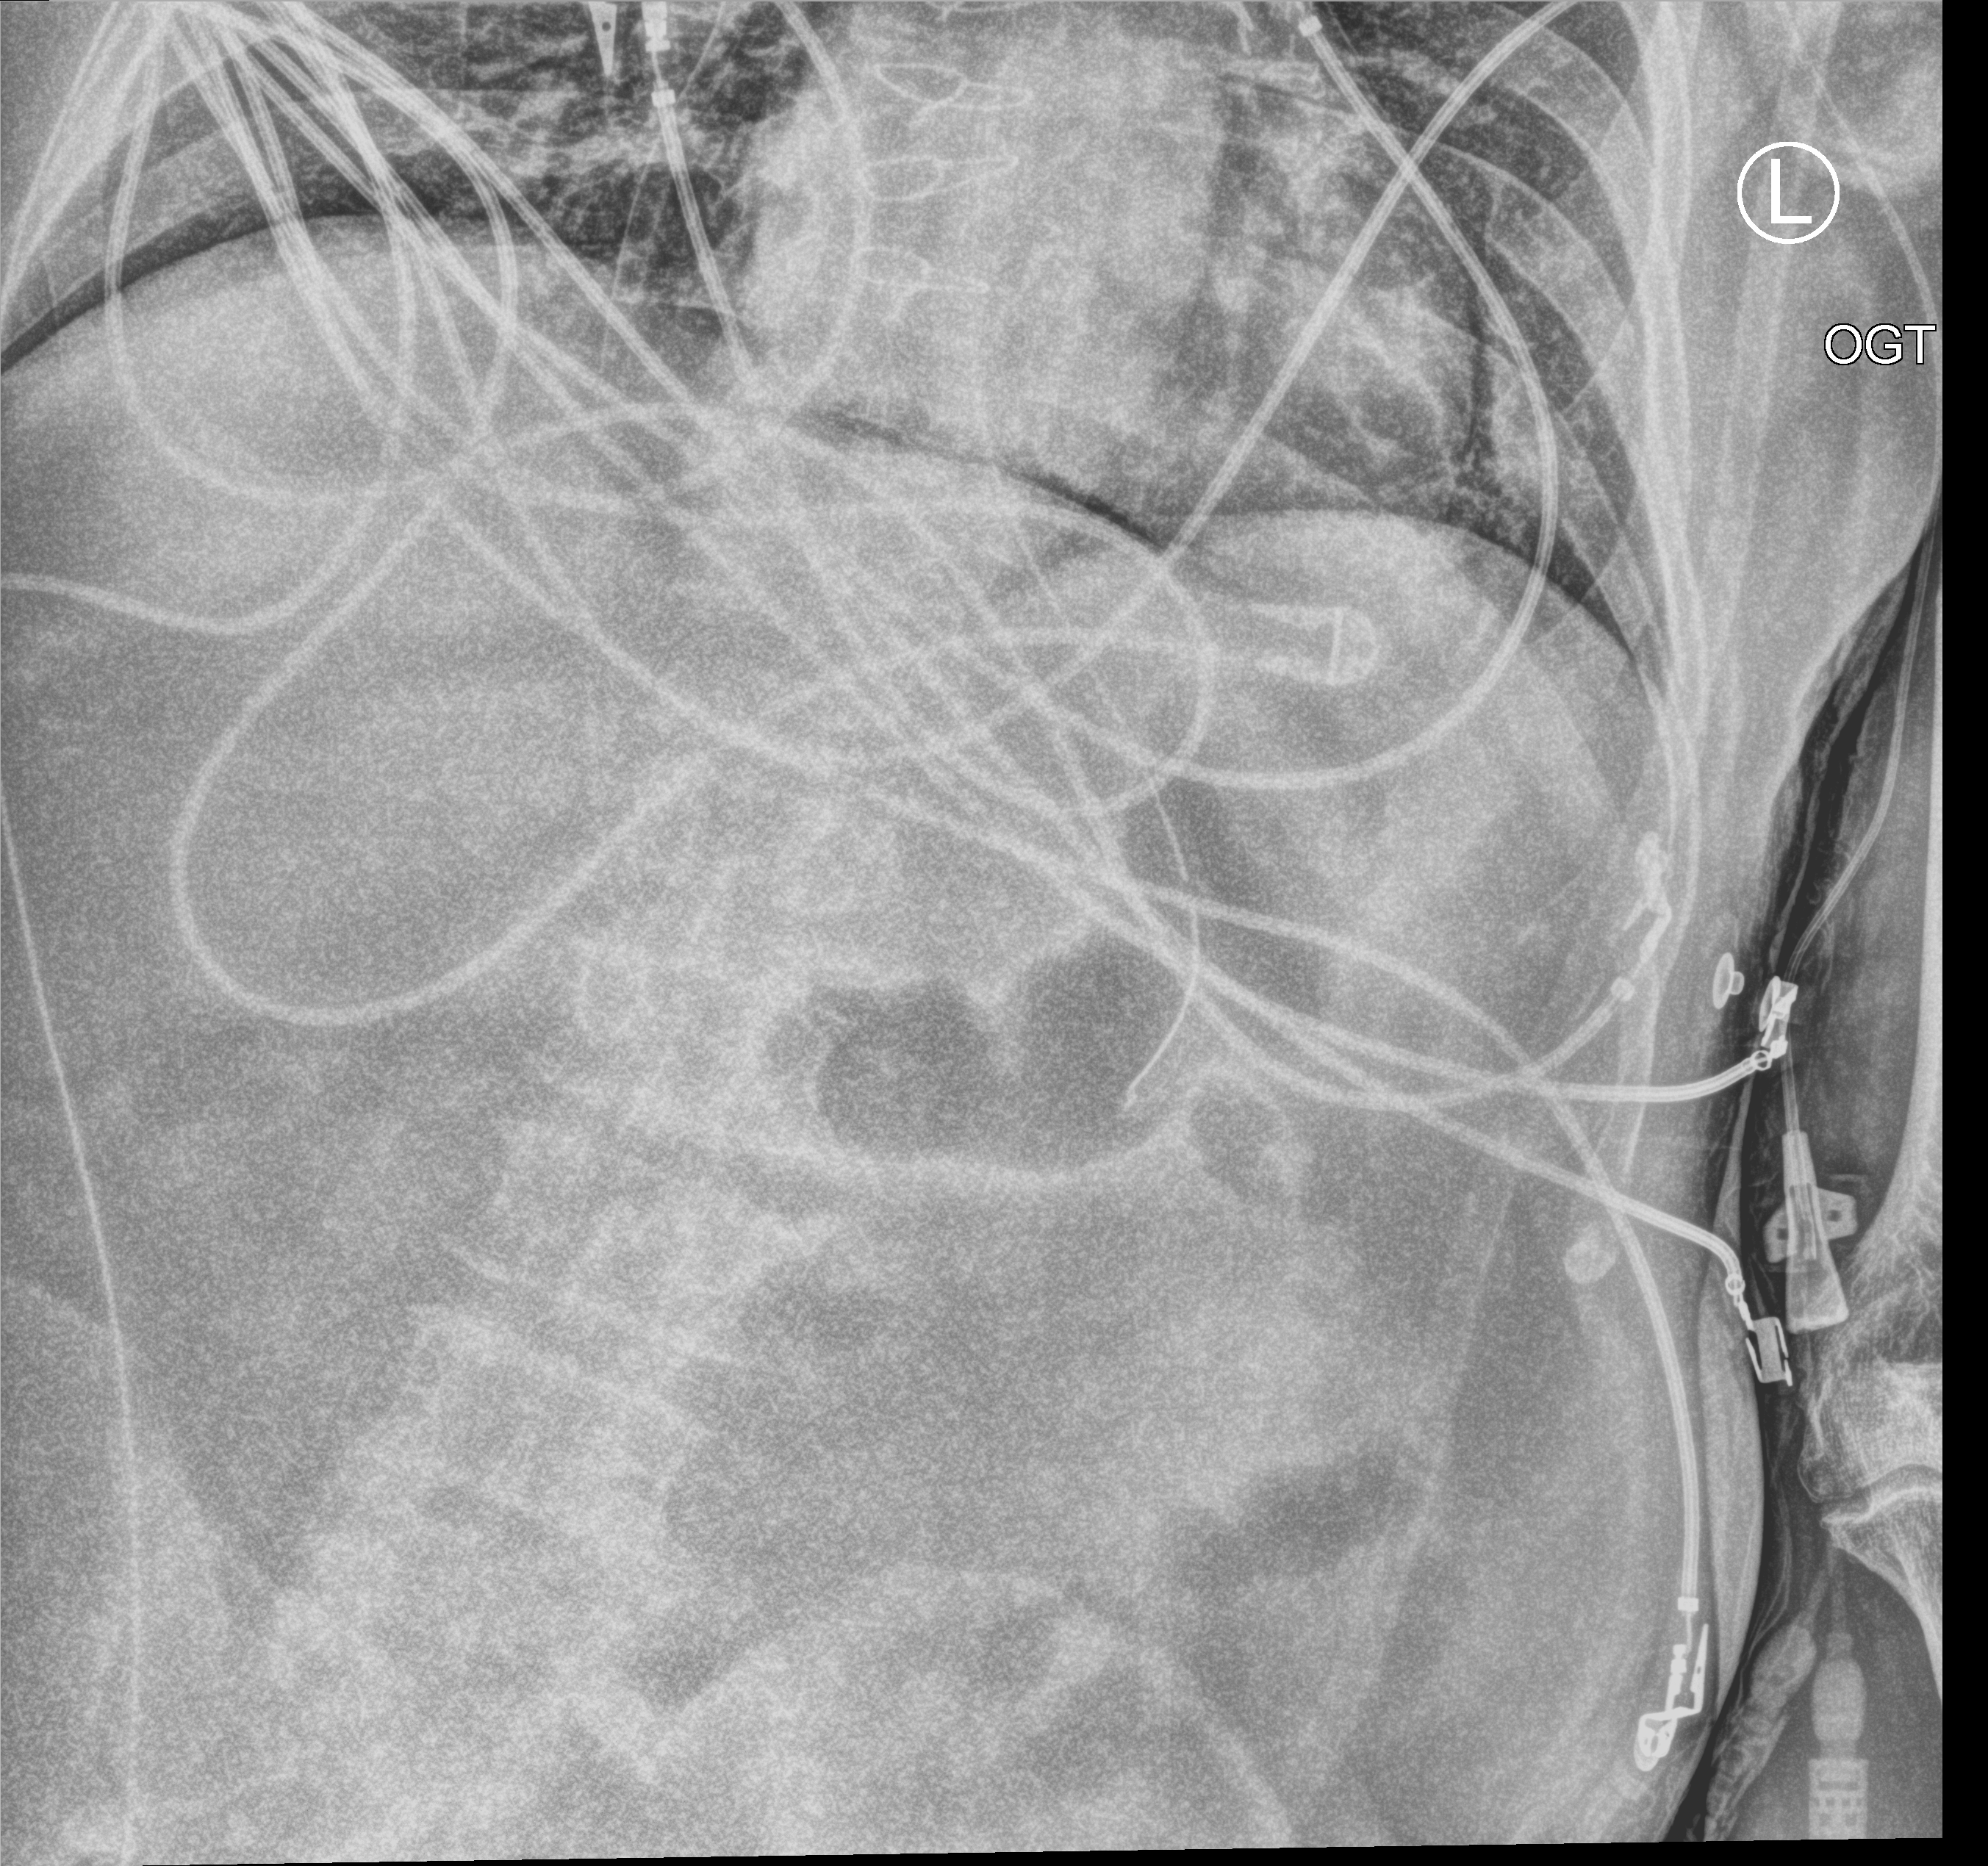
Portable chest radiograph; anteroposterior (AP) projection. Male patient hospitalised with COVID-19, age 60–74 years.
Admission-level facts for this patient (not findings on this image; timing relative to this image not recorded): other chronic lung disease (admission record): no; admitted to intensive care during this hospital stay: yes.